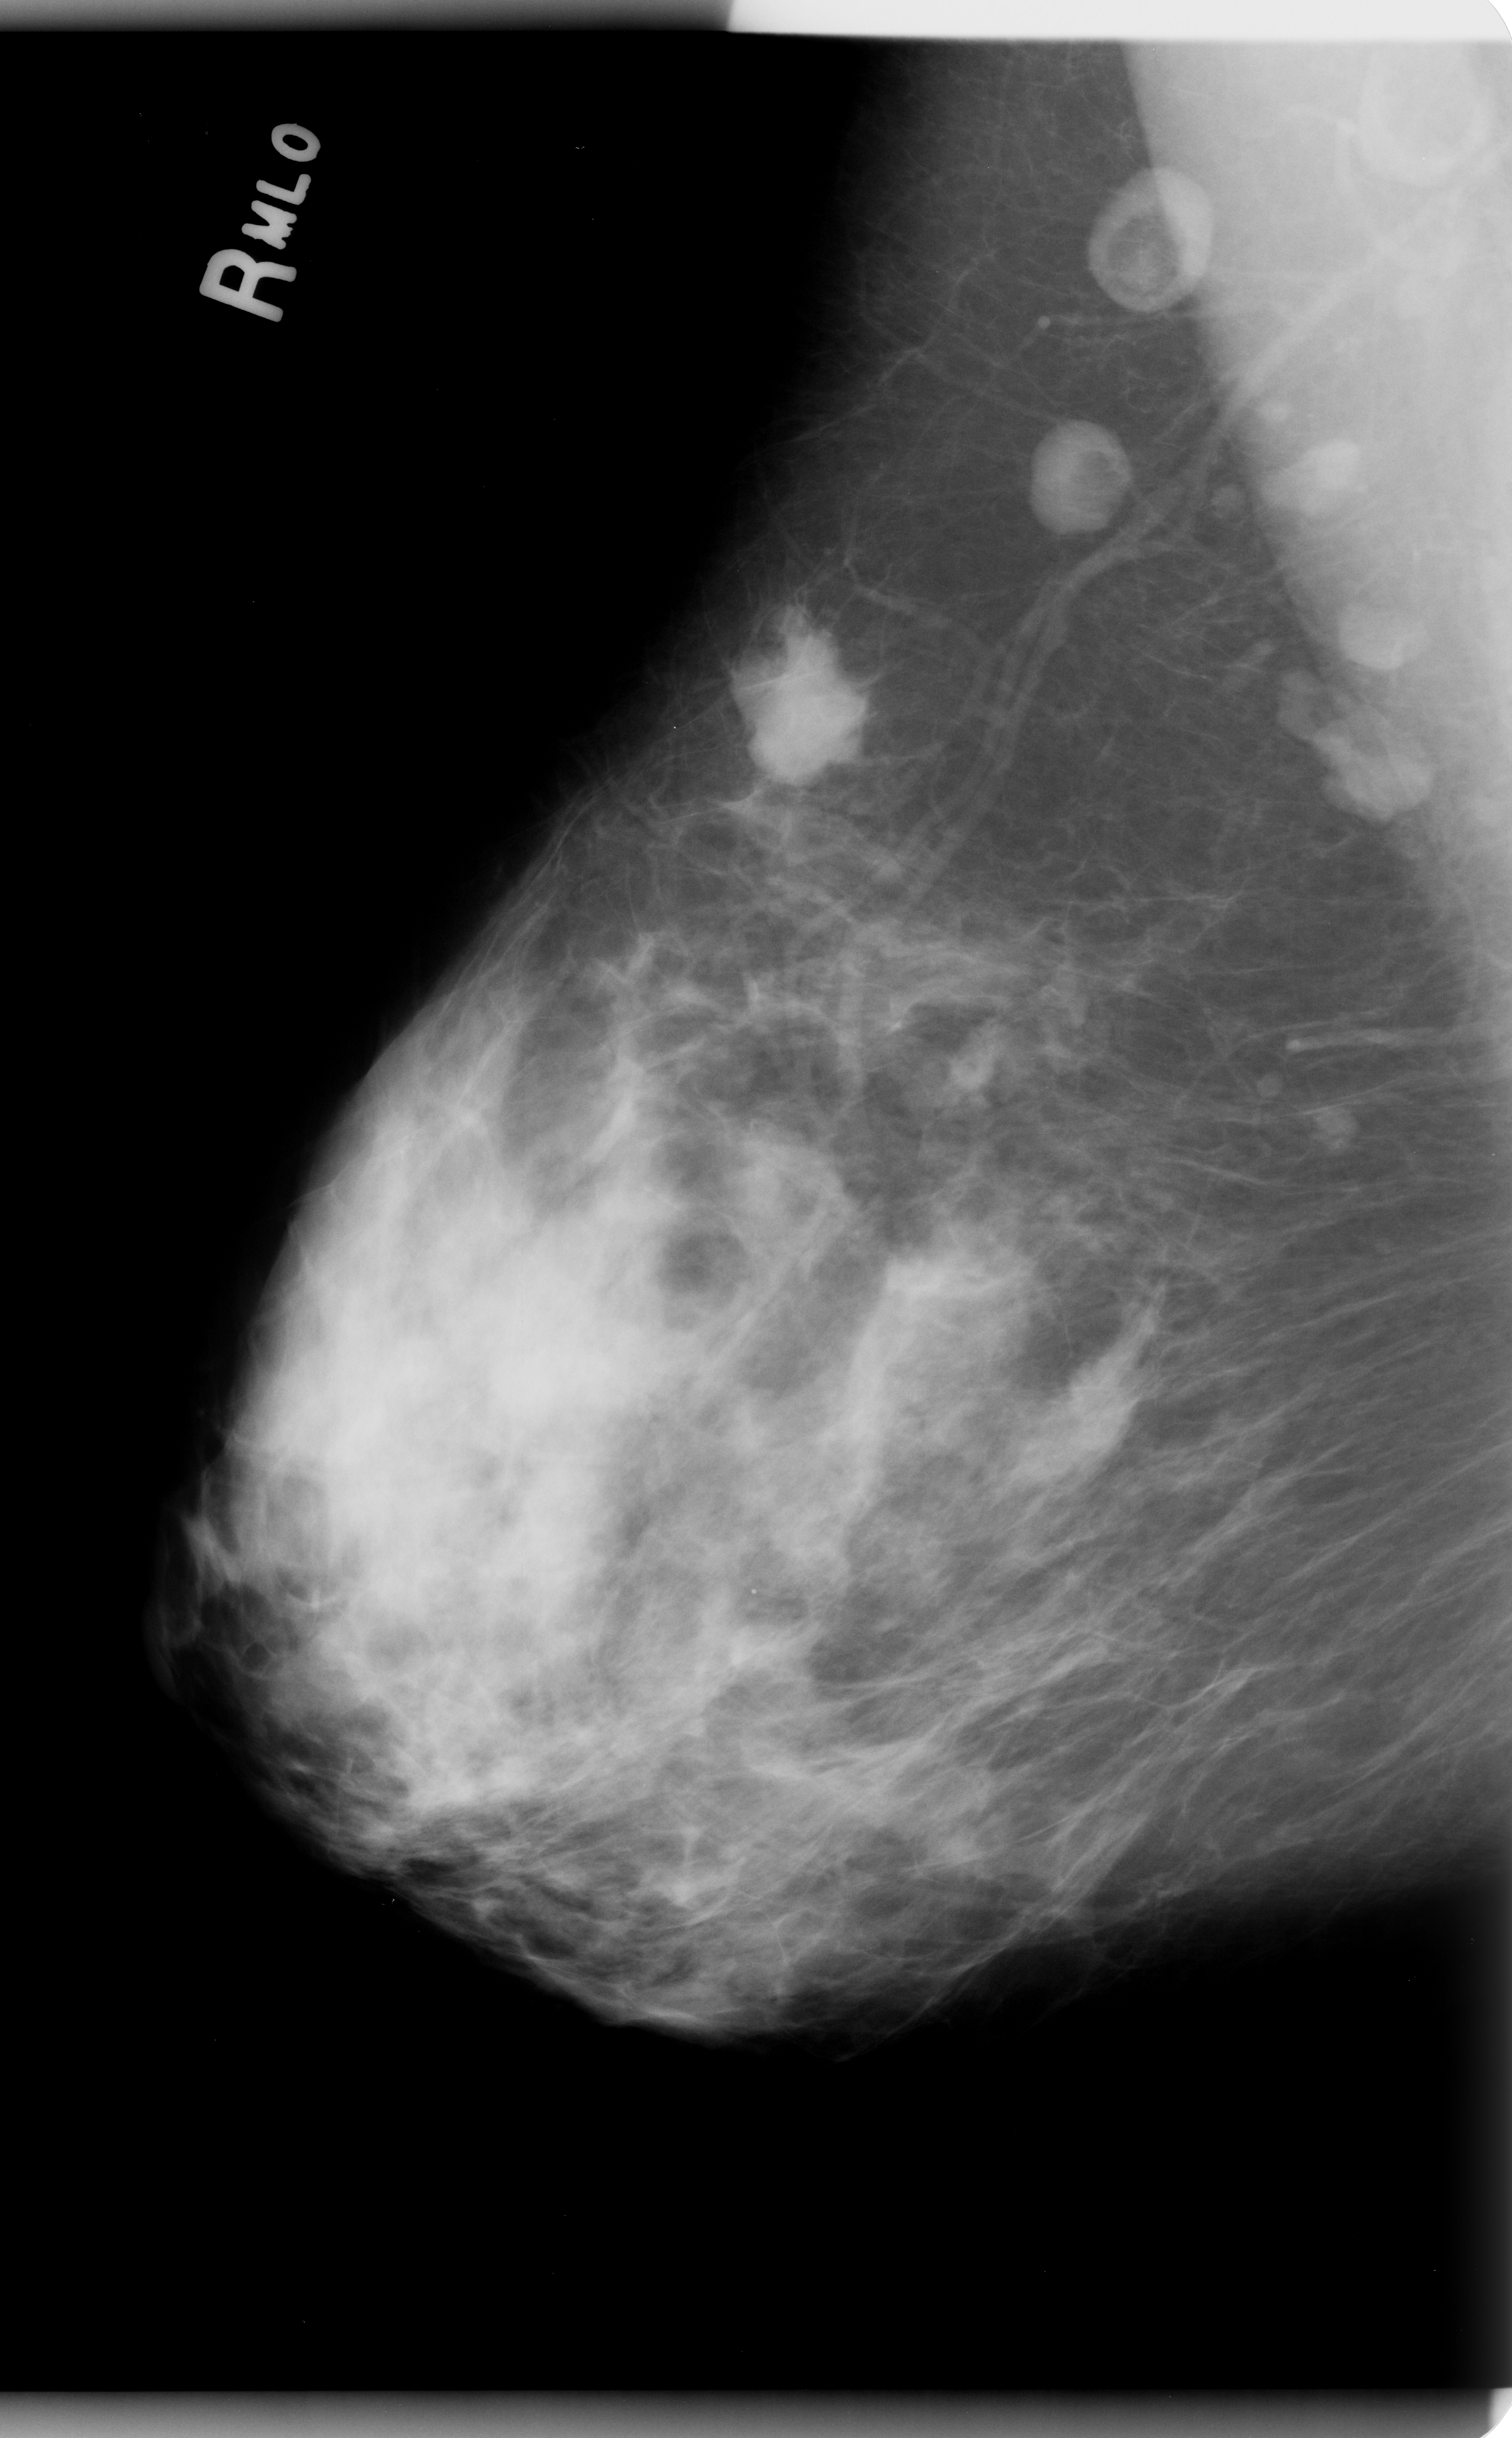
Digitized screen-film mammogram; right breast; MLO view; breast composition: heterogeneously dense (BI-RADS density category 3 of 4); 1512 × 2438 image matrix.
Marked abnormalities (boxes around the expert regions of interest):
- mass, shape irregular, margins microlobulated; BI-RADS assessment category 5; pathology result (as recorded, not read from the image): malignant: box from (x=731, y=620) to (x=881, y=808) px